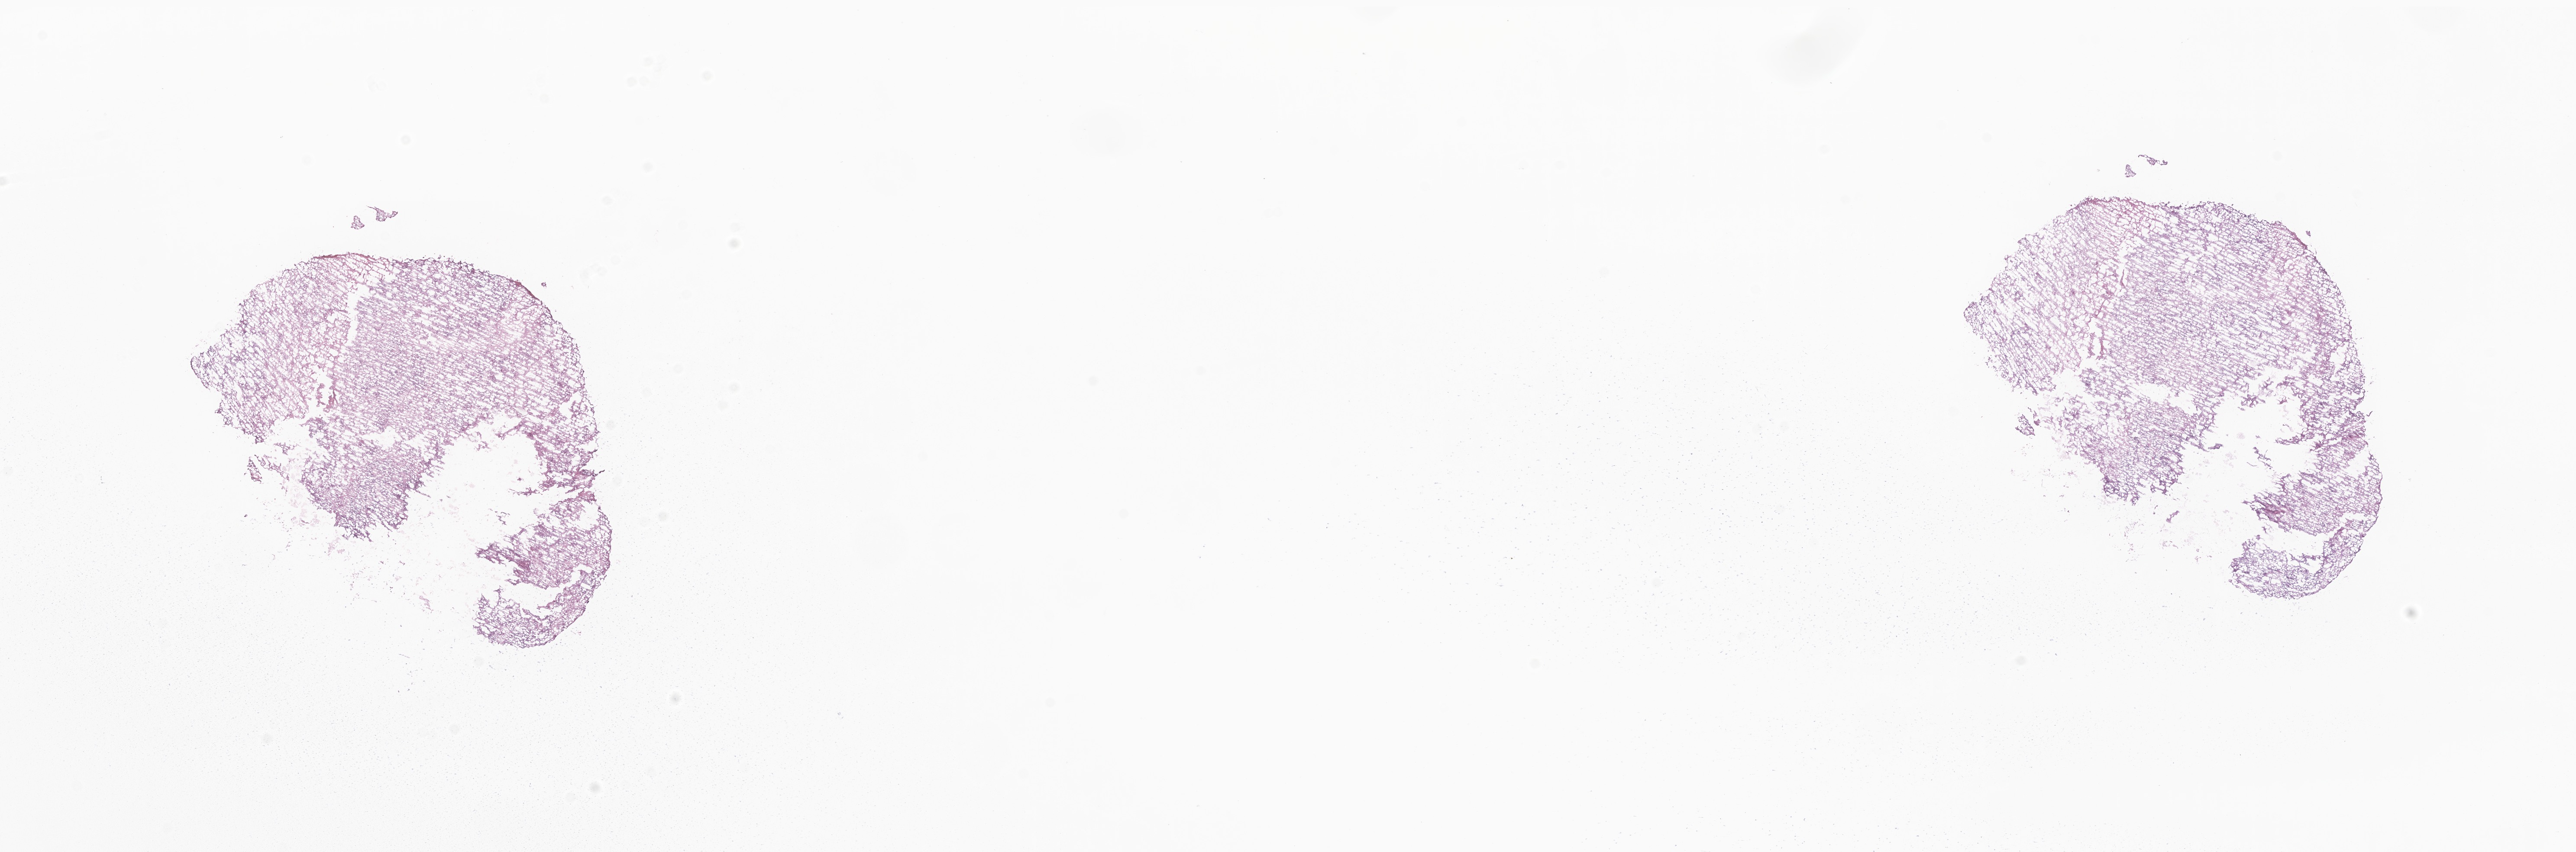
Digitized H&E-stained section of tumor tissue from the cerebellum — whole scanned area (about 25.1 x 8.3 mm) shown as a low-resolution overview; frozen section (OCT-embedded). Patient female; age 35 months (2 years 11 months).
* diagnosis: Ependymoma, NOS